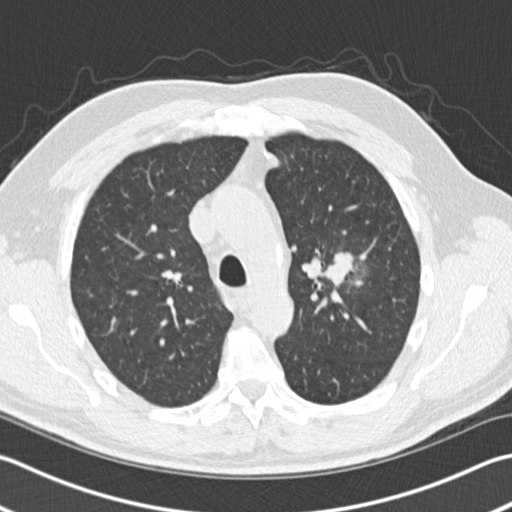
Chest CT (low-dose screening protocol), one axial image. Third screening round (two years after baseline). Lung window (W 1500 / L -600 HU). 2 mm slice thickness. Standard (soft-tissue) reconstruction kernel (B30f). Slice 45 of 153 in the series. 512 × 512 image matrix, field of view 346 × 346 mm. Male, age 65 years at enrolment. Former smoker at enrolment.
Lesion marked by an expert reader, bounding box (x1, y1, x2, y2) in pixels: (306, 240, 370, 304). The screening reader recorded 4 non-calcified nodules or masses ≥4 mm on this exam (left upper lobe, left upper lobe, left lower lobe, right middle lobe); which of them this box marks is not recorded. Official screen result: positive, other. Later outcome: lung cancer diagnosed 196 days after this screen — acinar cell carcinoma, left upper lobe, stage IA (AJCC 6th edition), 25 mm at pathology.